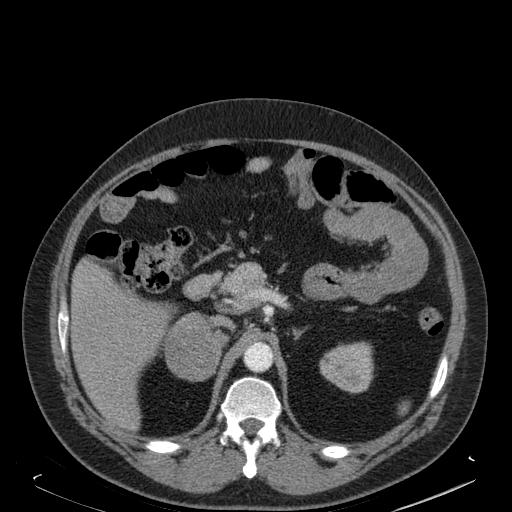
Contrast-enhanced abdominal CT, one axial slice; slice 112 of 181 in the series (ordered by position); soft-tissue window (W 400 / L 40 HU); 1.5 mm slice thickness; 512 × 512 image matrix. Male patient. From the clinical record (not read from this slice): diagnosis: adrenocortical carcinoma; tumour side: right adrenal; tumour size at pathology: 7.5 cm; Ki-67 index: 25 %; stage (as recorded): 4.
Annotated regions visible in this slice (semi-automatically segmented with operator editing):
- mass: bounding box (x1, y1, x2, y2) in pixels: (166, 314, 217, 380)